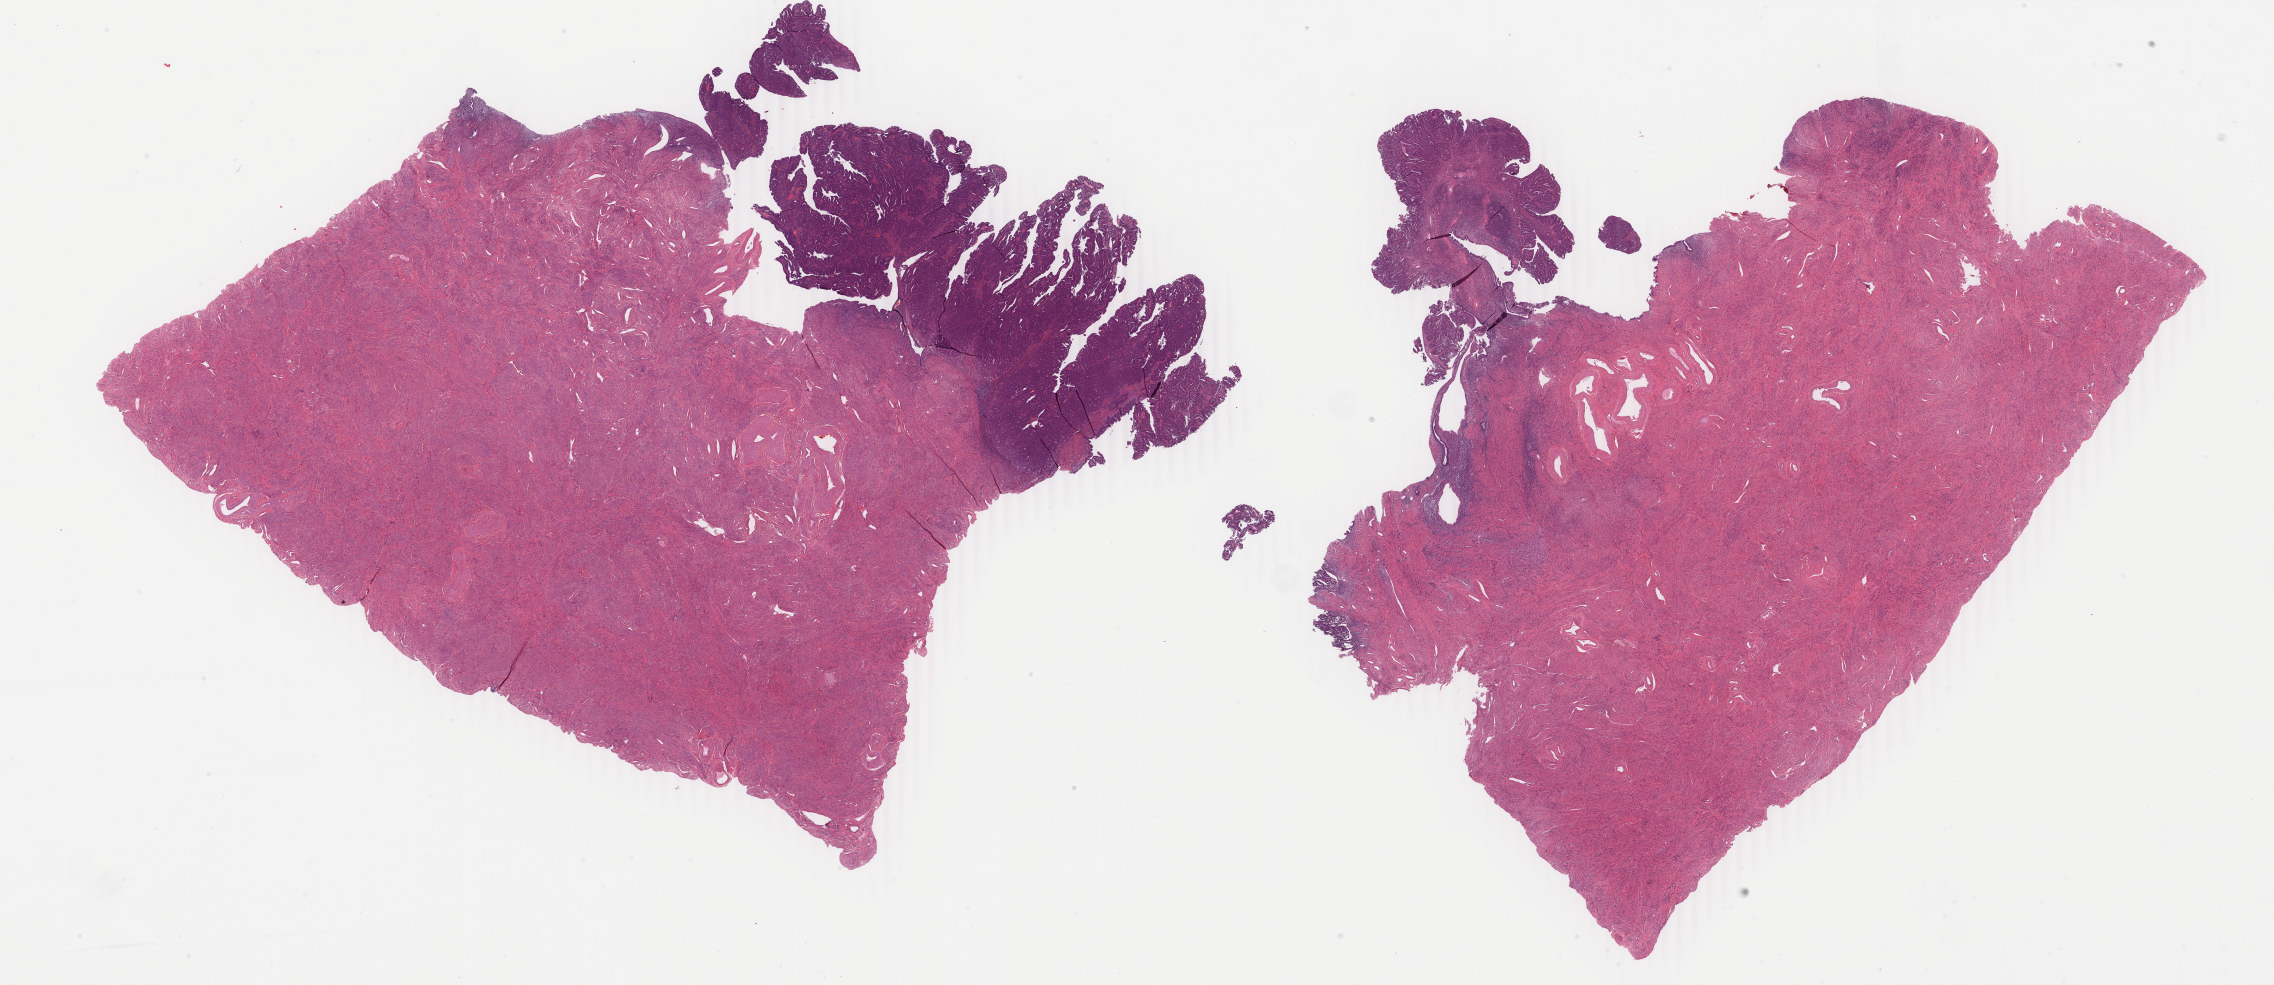
Digitized H&E tissue section (whole slide) — shown as a low-resolution overview of the whole scanned area (about 36.2 x 15.7 mm), formalin-fixed paraffin-embedded (FFPE) diagnostic section, sample: primary tumour, uterus. Female, age 56 years at initial diagnosis.
Histologic diagnosis: Endometrioid adenocarcinoma, NOS (endometrium).